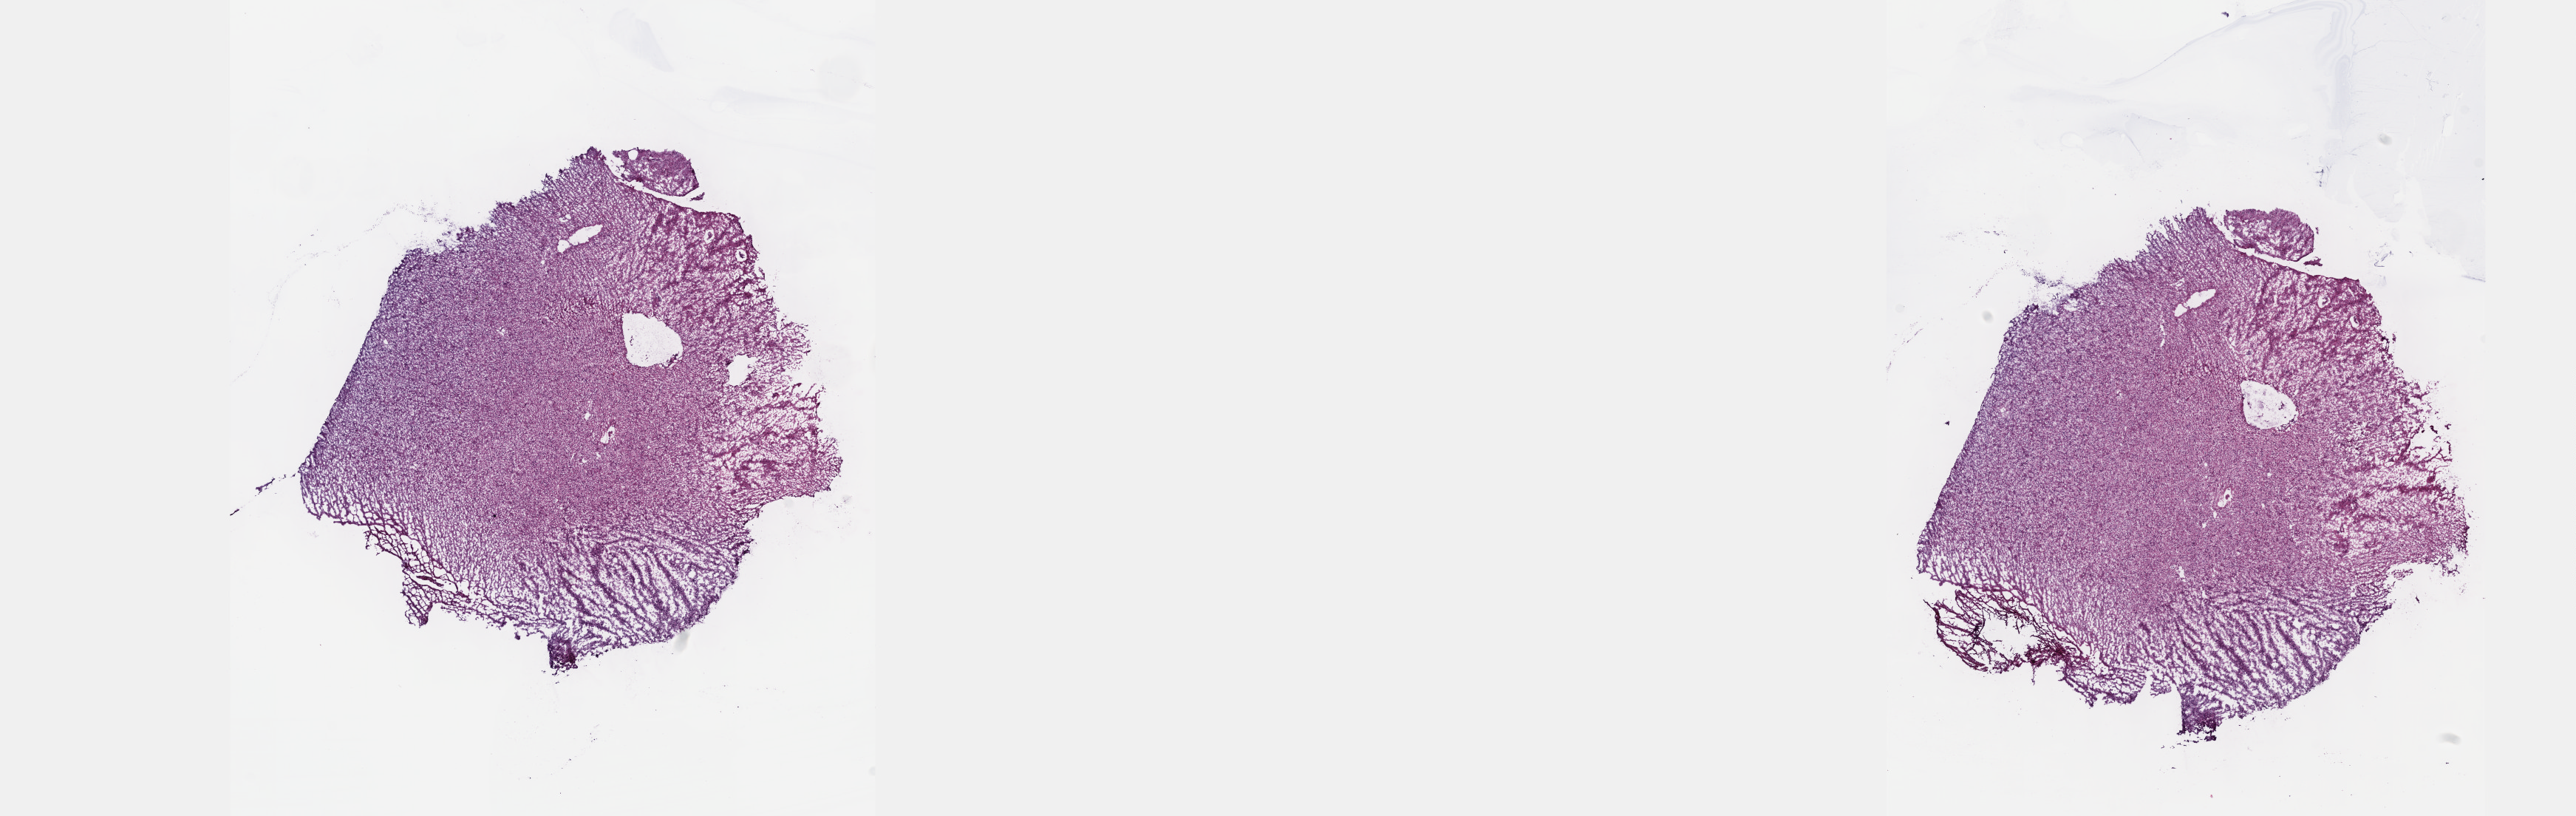
Whole-slide histology image, H&E-stained — whole scanned area (about 28.2 x 8.9 mm, from a 40x scan) shown as a low-resolution overview, frozen section, sample: primary tumour, brain. Patient: female, age at initial diagnosis 61 years. Histologic grade: G3 (poorly differentiated). Pathologist review of this section (percent, as recorded): tumour cells 45%, tumour nuclei 80%, normal cells 10%, stromal cells 45%, necrosis 0%. Inflammatory infiltration, as recorded: lymphocyte infiltration 0%, monocyte infiltration 0%, neutrophil infiltration 0%.
Histologic diagnosis: Oligodendroglioma, anaplastic. Laterality: right.